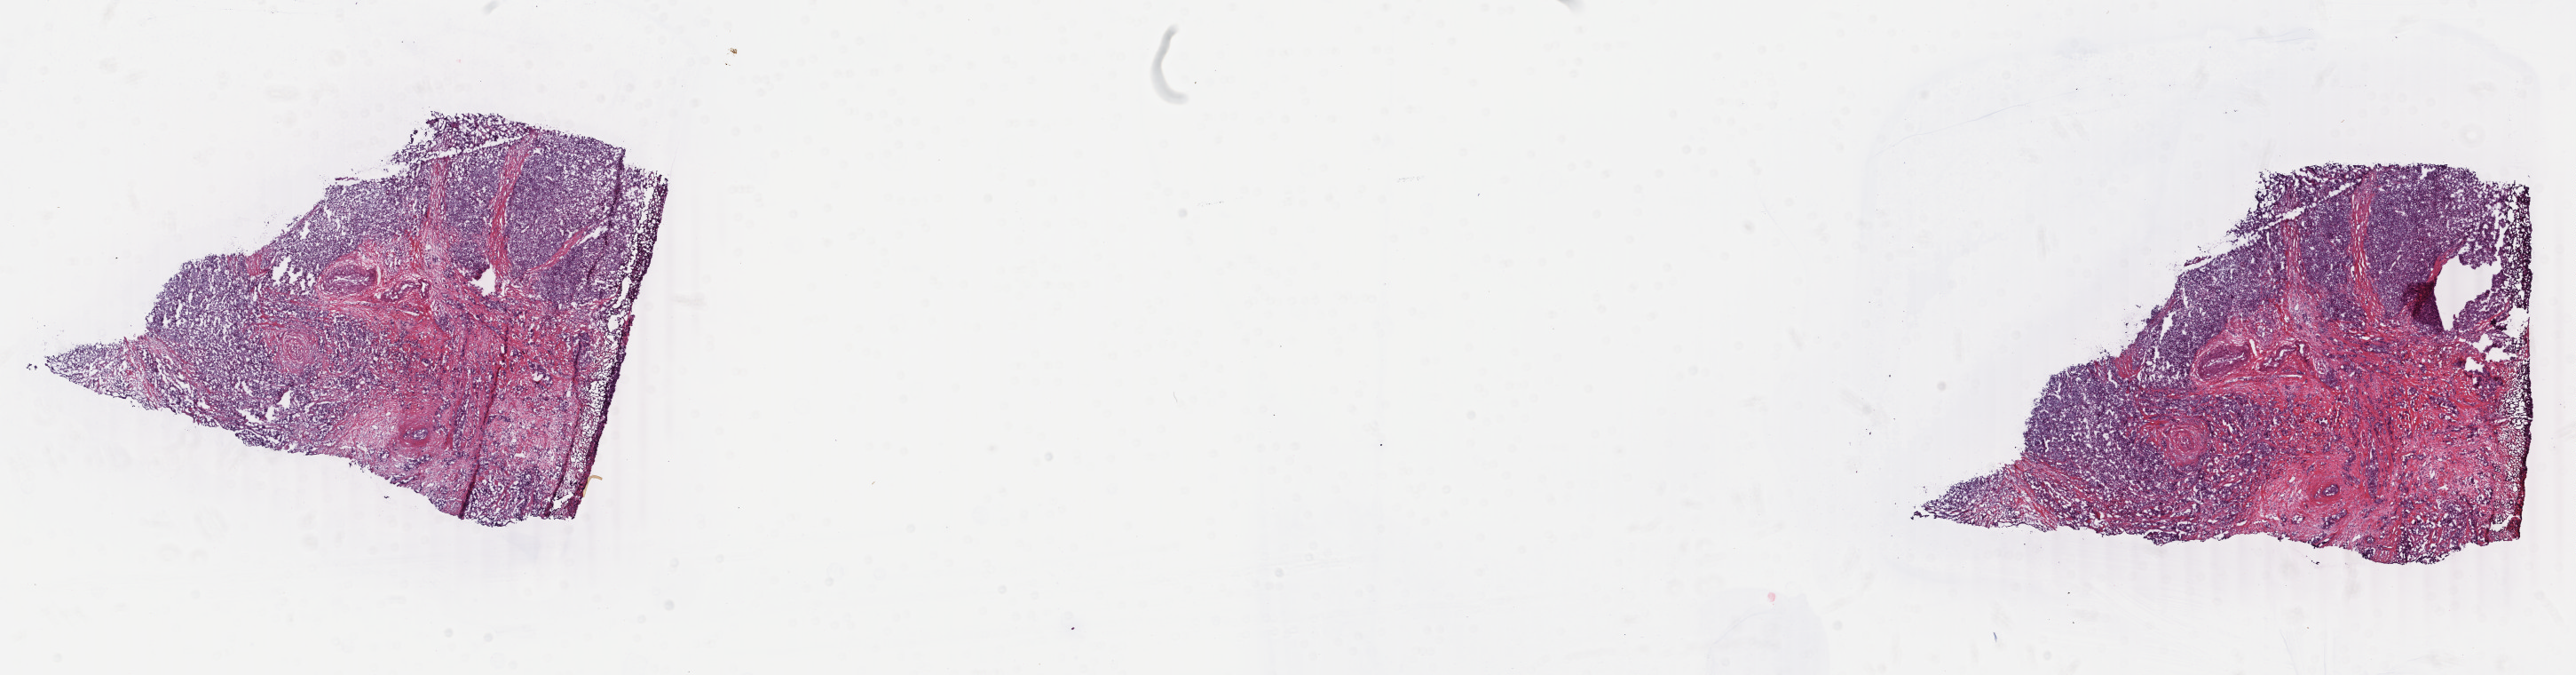
Digitized H&E-stained tissue section (whole slide) — low-resolution overview of the scanned area, about 23.1 x 6.0 mm, frozen section, sample: primary tumour, breast. Patient: female, age at initial diagnosis 66 years.
Histologic diagnosis: Infiltrating duct carcinoma, NOS.